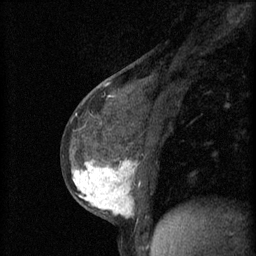
Breast MRI (dynamic contrast-enhanced), one sagittal slice; position 26 of 60 along the scan axis; 3 images stored at this slice position (order not interpretable as contrast timing); 1.5 T; TE 4.2 ms, TR 11 ms; 2 mm slice thickness; 256 × 256 image matrix, field of view 180 × 180 mm. Patient: female, 37 years.
Structures marked on this image (semi-automatically segmented with operator editing):
- analysis volume of interest (the breast-tissue region the enhancement analysis was run in; not a lesion): bounding box <65,138,174,221> (left, top, right, bottom; pixels)
- tumour enhancement mask (voxels above the 70 % enhancement threshold inside the analysis volume of interest): <73,160,140,217>